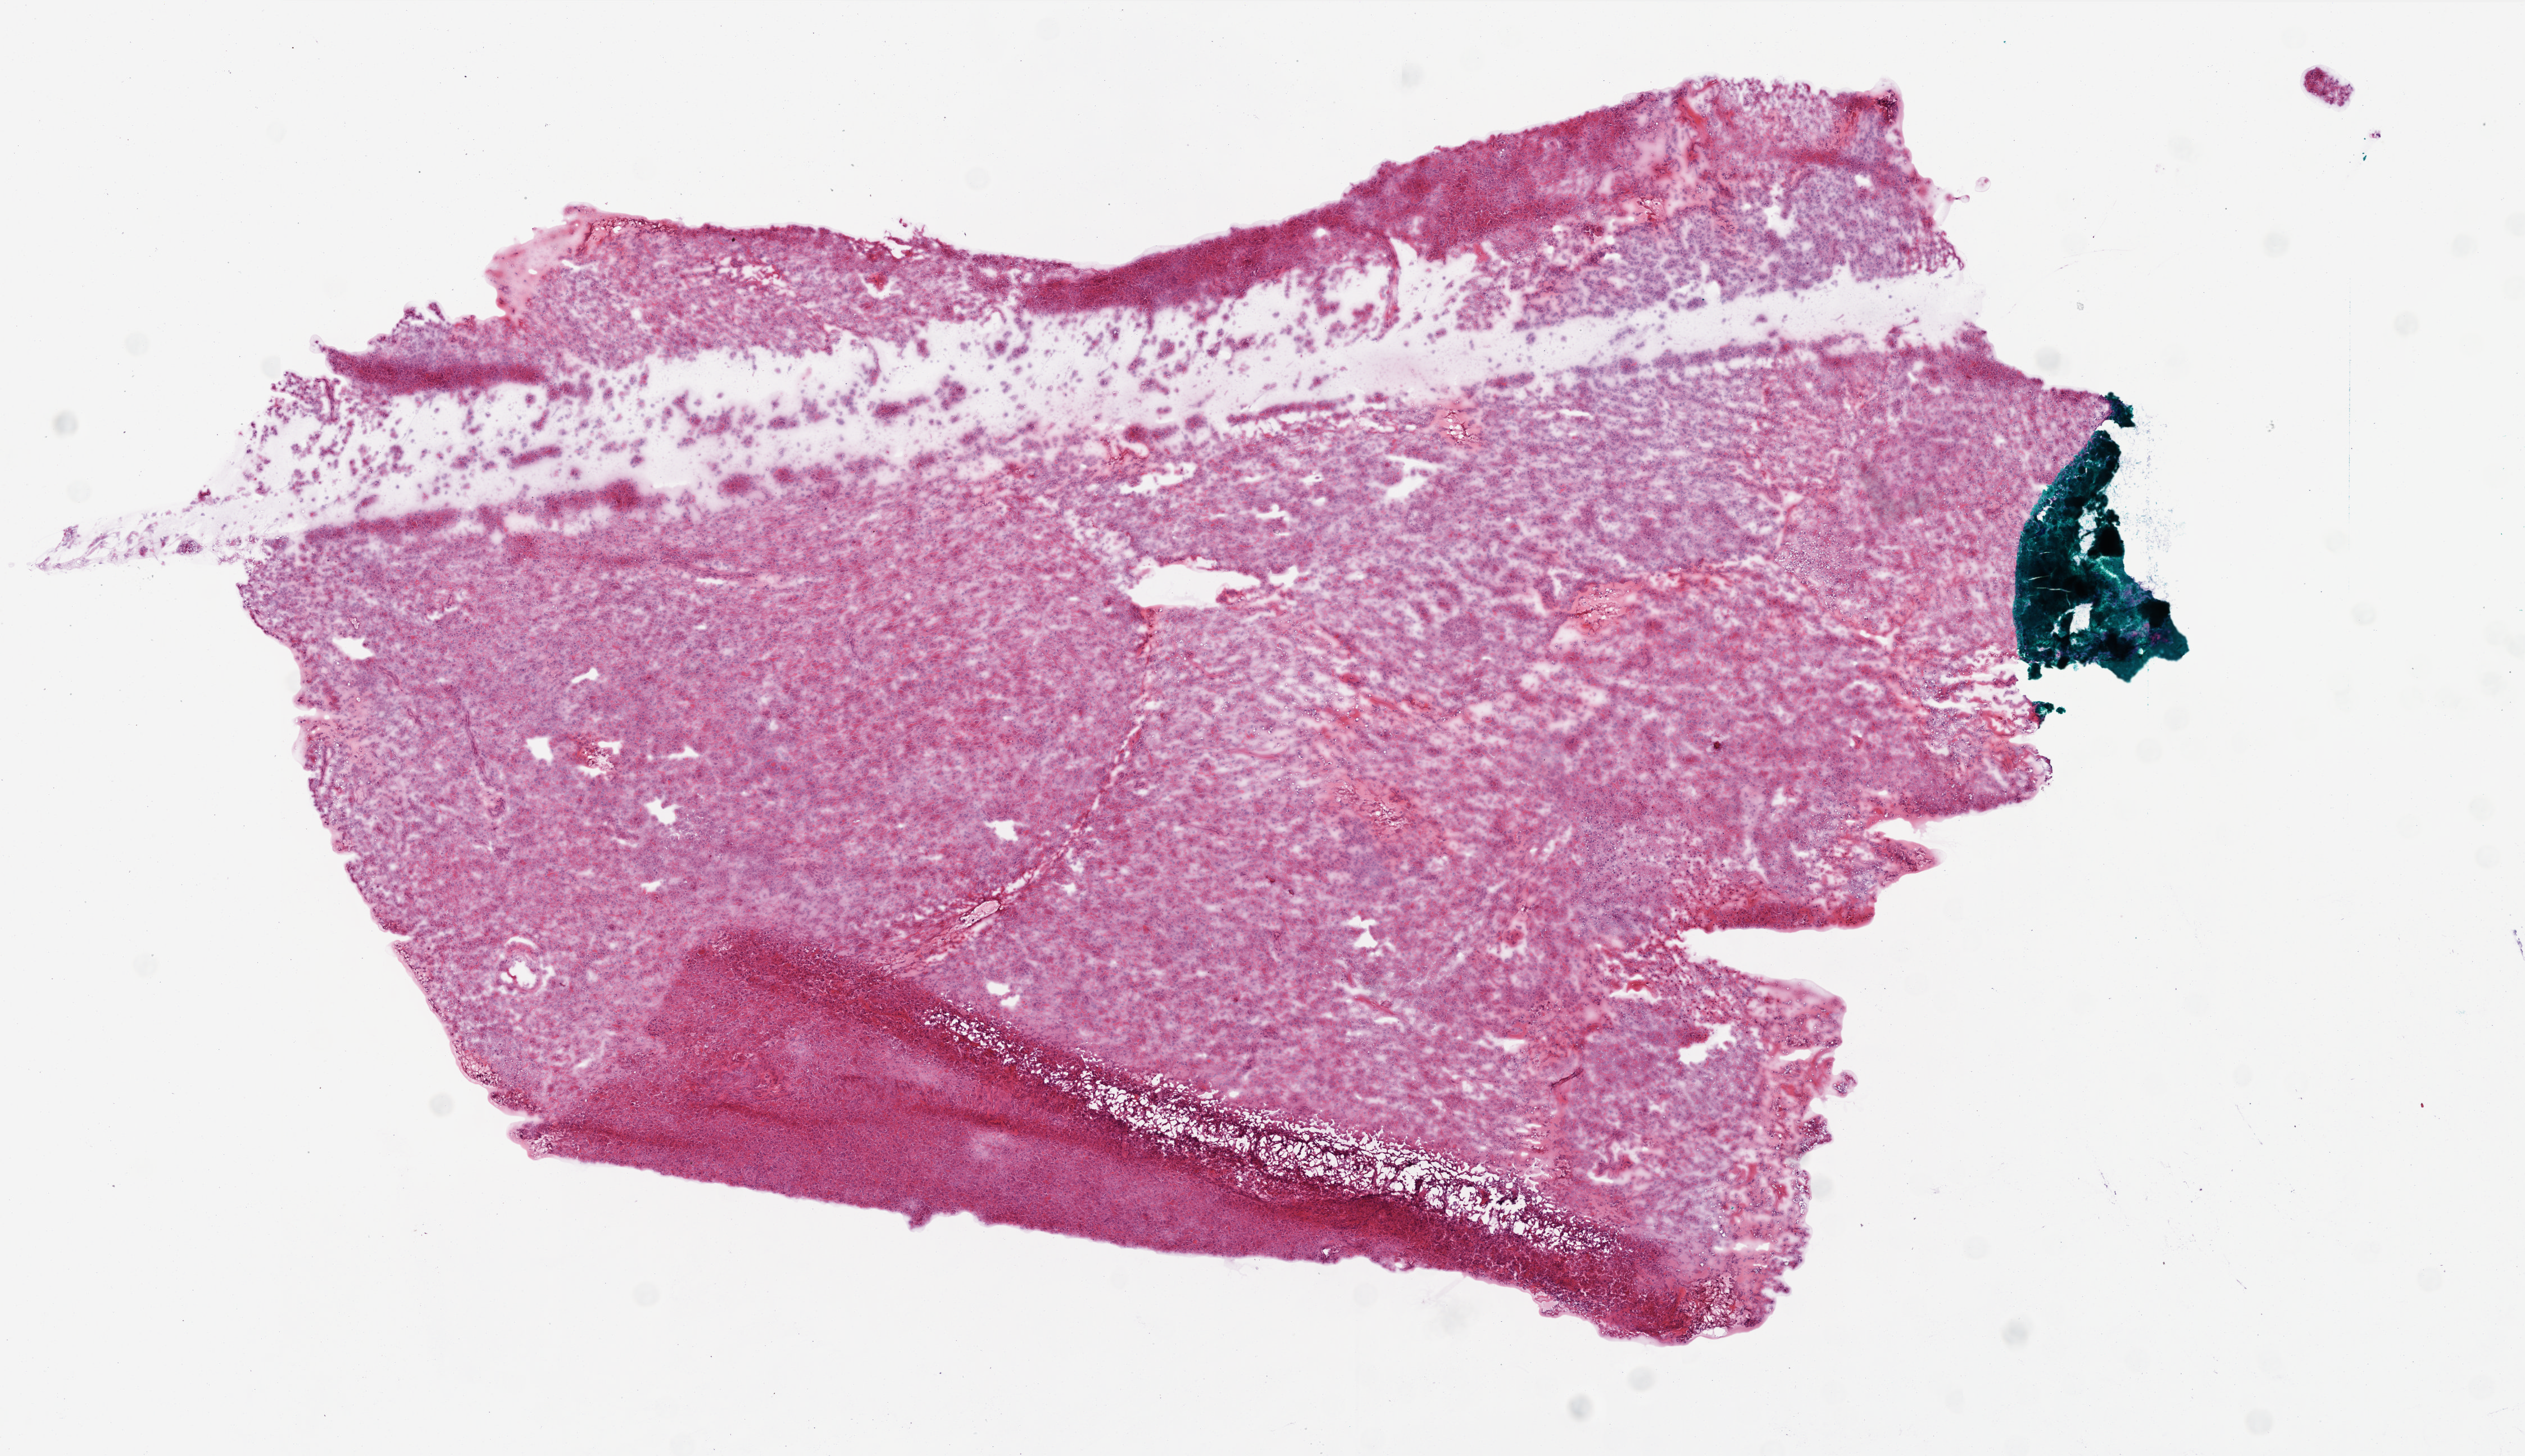
H&E-stained whole-slide image, whole scanned area (about 9.0 x 5.2 mm) shown as a low-resolution overview, frozen section, sample: primary tumour, brain. Female, age 74 years at initial diagnosis. Pathologist review of this section (percent, as recorded): tumour cells 95%, tumour nuclei 100%, normal cells 0%, stromal cells 0%, necrosis 5%.
- pathologic diagnosis: Glioblastoma